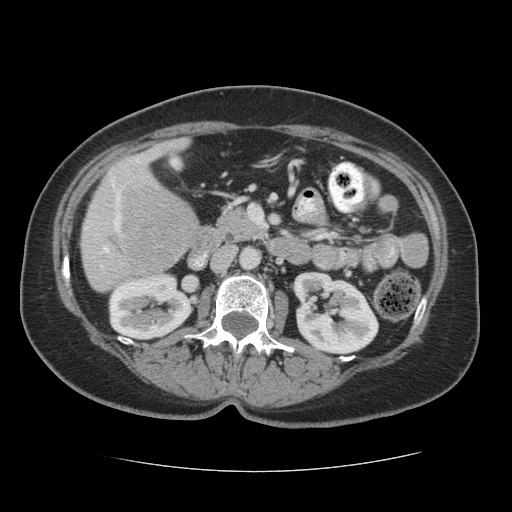
Contrast-enhanced abdominal CT (liver protocol), one axial slice. Position 17 of 75 along the scan axis. Reconstruction kernel STANDARD. Soft-tissue window (W 400 / L 40 HU). 512 × 512 image matrix. From the clinical record (not read from this slice): diagnosis: hepatocellular carcinoma (patient treated with transarterial chemoembolisation; whether this scan precedes or follows treatment is not stated here); TNM stage (as recorded): Stage-I; Child-Pugh class: A; tumour nodularity: uninodular.
Structures marked on this image (semi-automatic segmentation, software-assisted and operator-edited):
- liver parenchyma outside the tumour (the mass and vessels are separate outlines, so this box may not span the whole liver): bounding box <80,142,196,292> (left, top, right, bottom; pixels)
- mass: <110,171,200,274>
- liver vessels: <84,158,140,267>